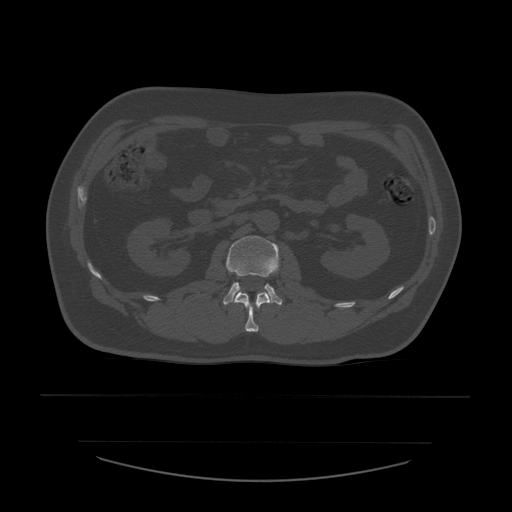
CT including the spine, one axial slice; slice 212 of 532 in the series (ordered by position); reconstruction kernel STANDARD; bone window (W 1800 / L 400 HU); 1.25 mm slice thickness; 512 × 512 image matrix, field of view 441 × 441 mm. Patient age 44 years. Case-level facts recorded for this patient, not image findings: primary cancer: soft tissue sarcoma.
Structures marked on this image (semi-automatically segmented with operator editing):
- L1 vertebra: box from (x=234, y=292) to (x=272, y=332) px
- L2 vertebra: (x=223, y=236)–(x=283, y=306)